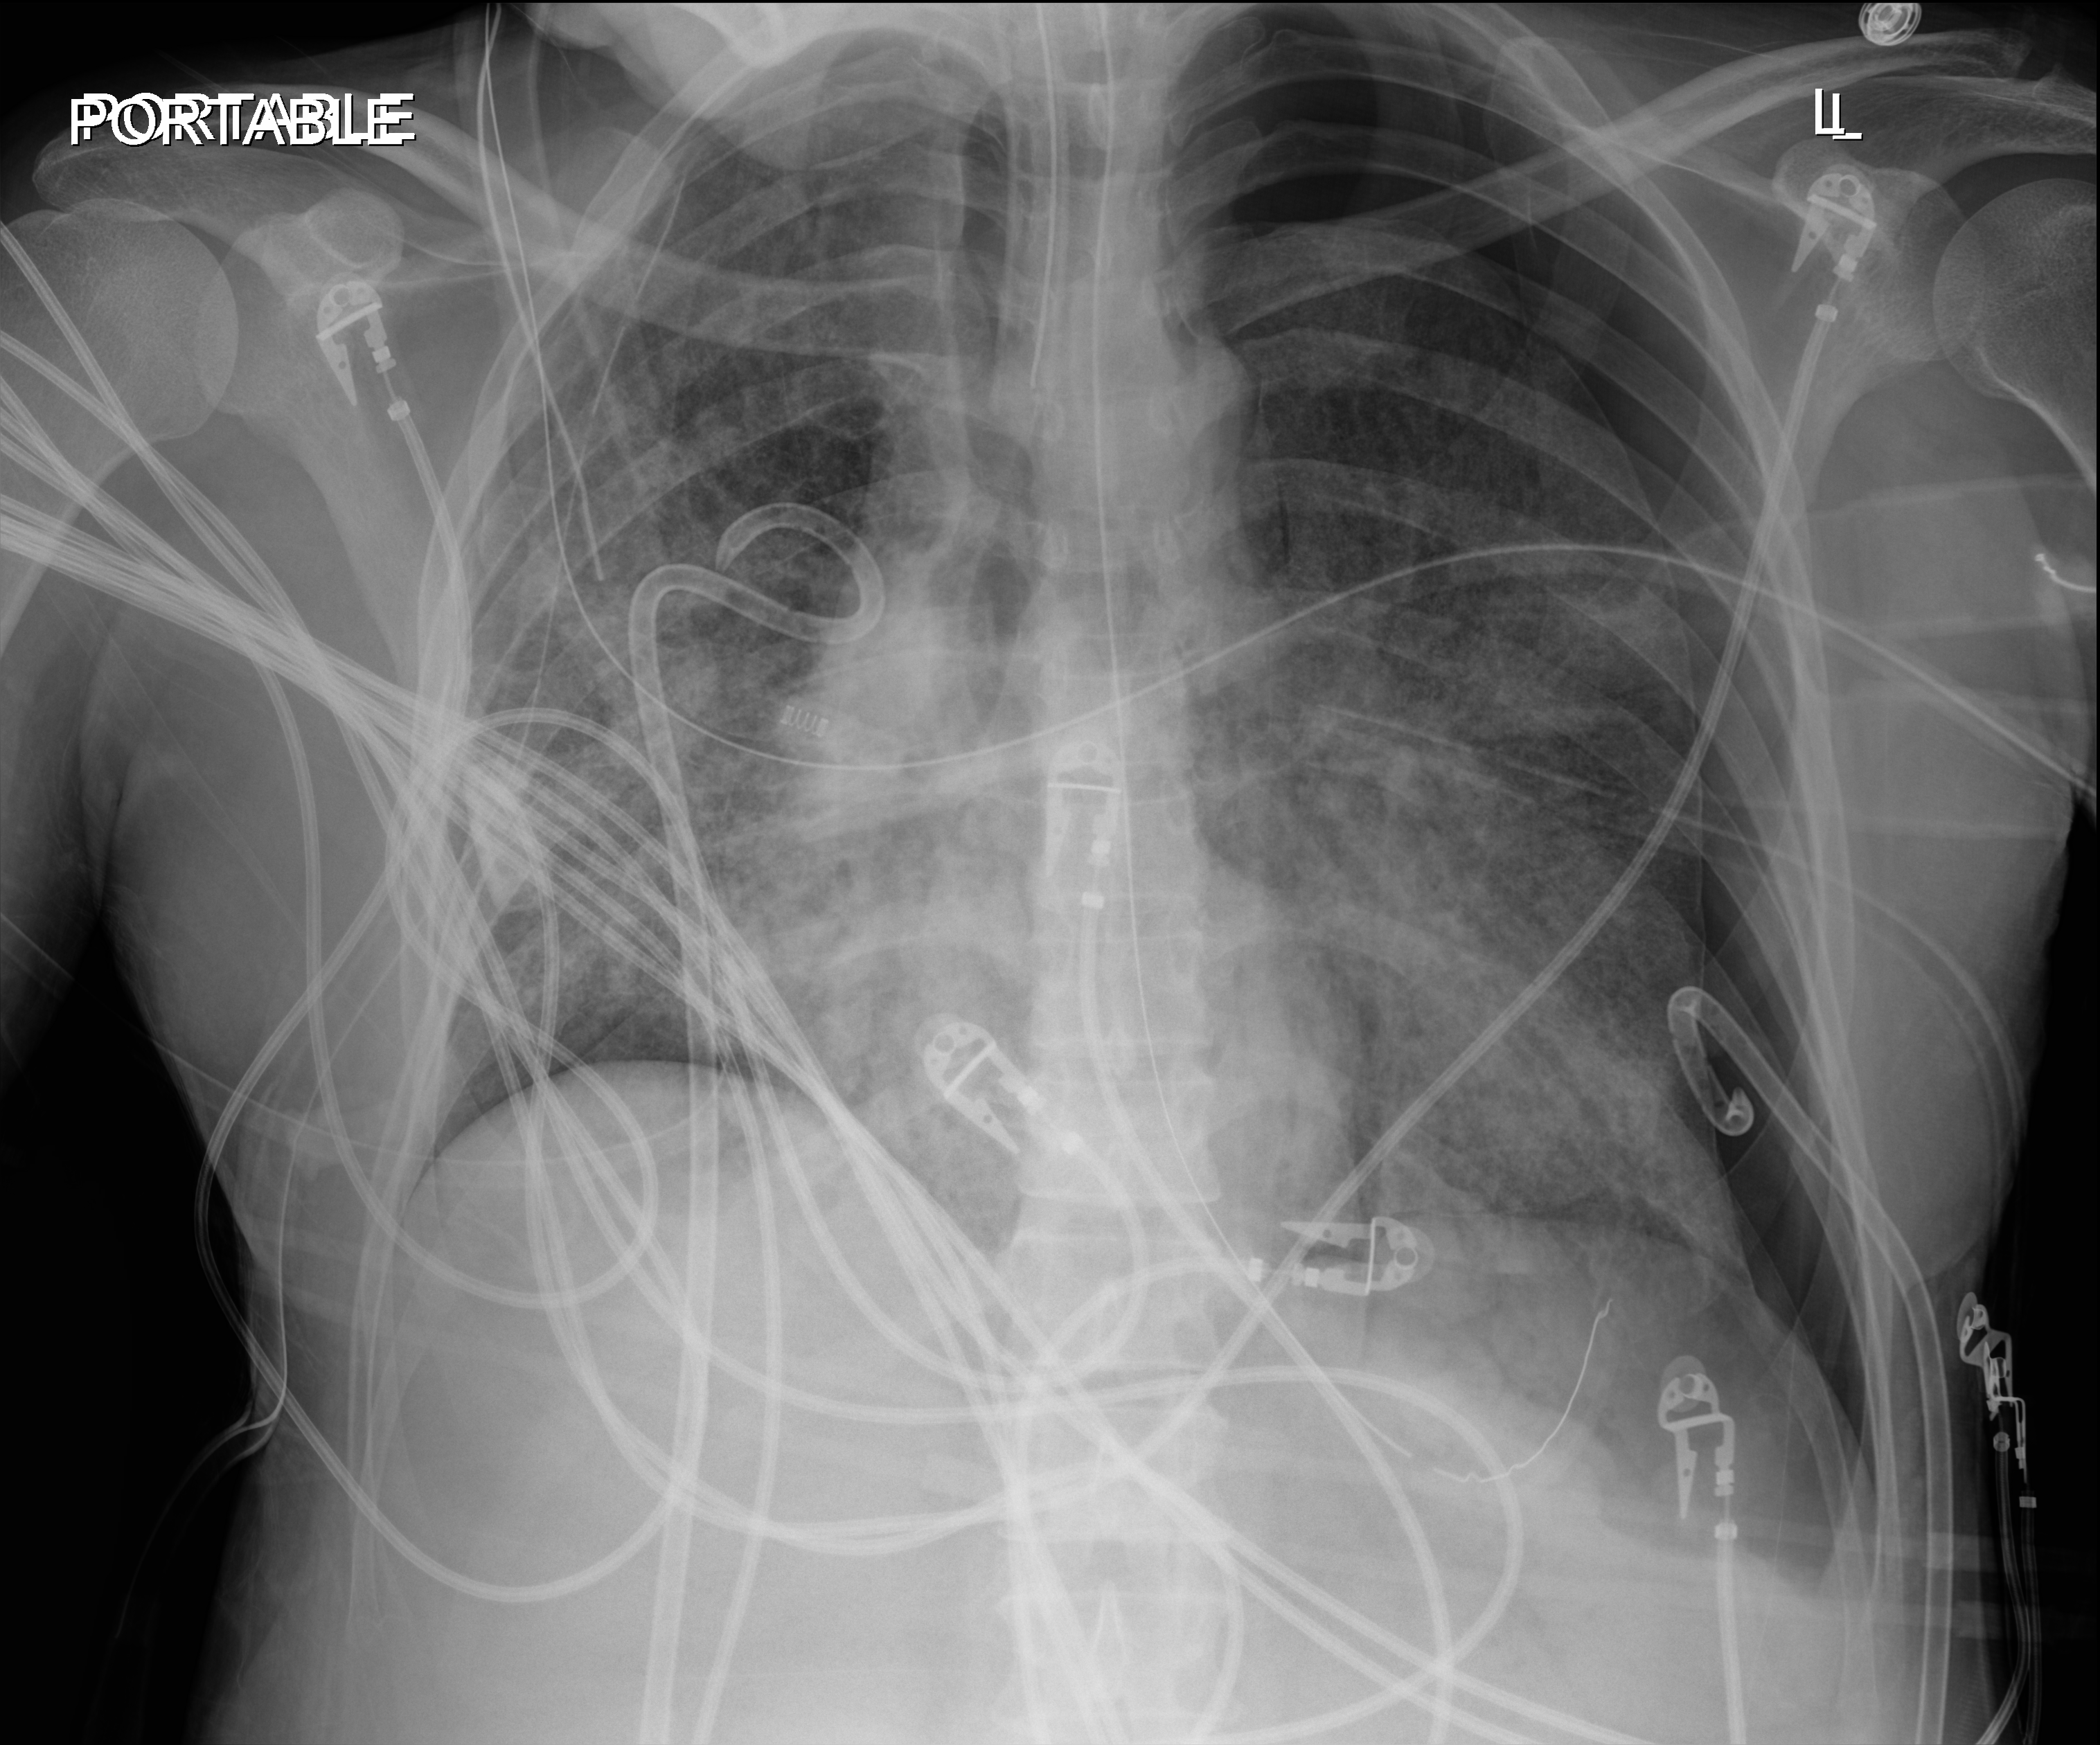
Chest X-ray, anteroposterior (AP) projection. Patient hospitalised with COVID-19, aged 18–59 years.
From the hospital-stay record, not from the radiograph (when in the stay this image was taken is not recorded):
- mechanically ventilated during this hospital stay: yes